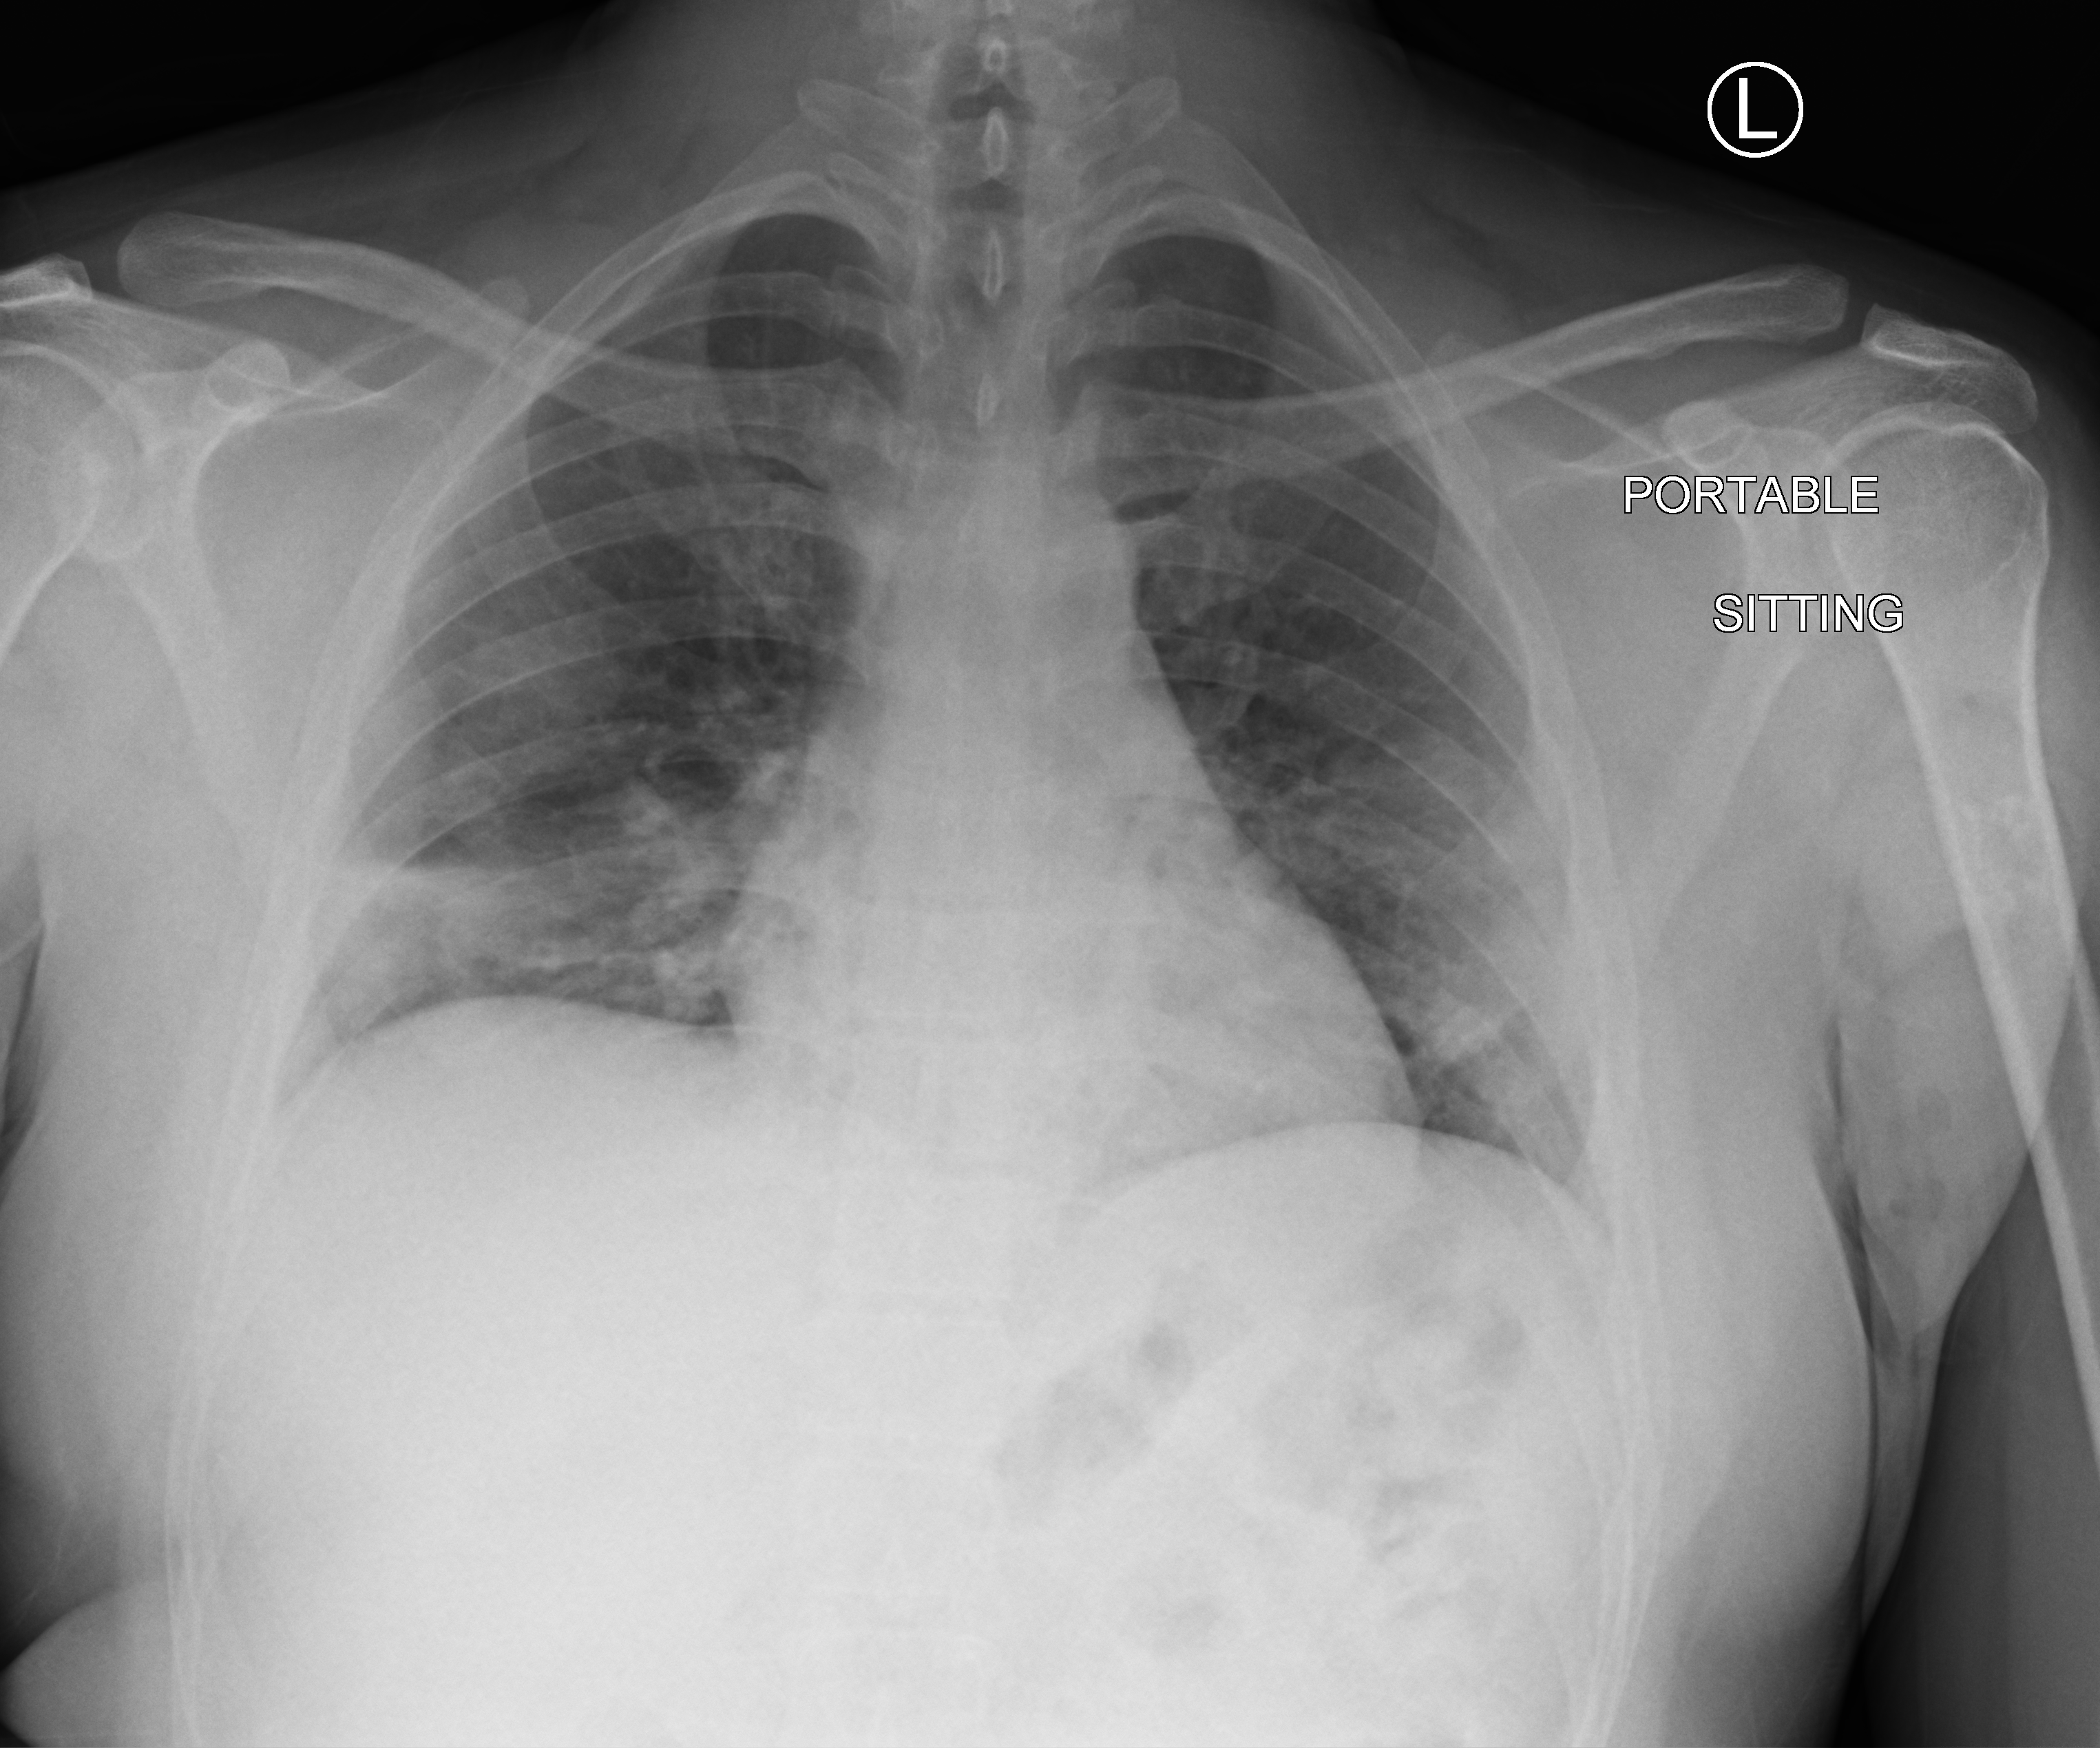
Chest X-ray (portable). Patient hospitalised with COVID-19; male, aged 18–59 years.
Admission-level facts for this patient (not findings on this image; timing relative to this image not recorded): admitted to intensive care during this hospital stay: no.